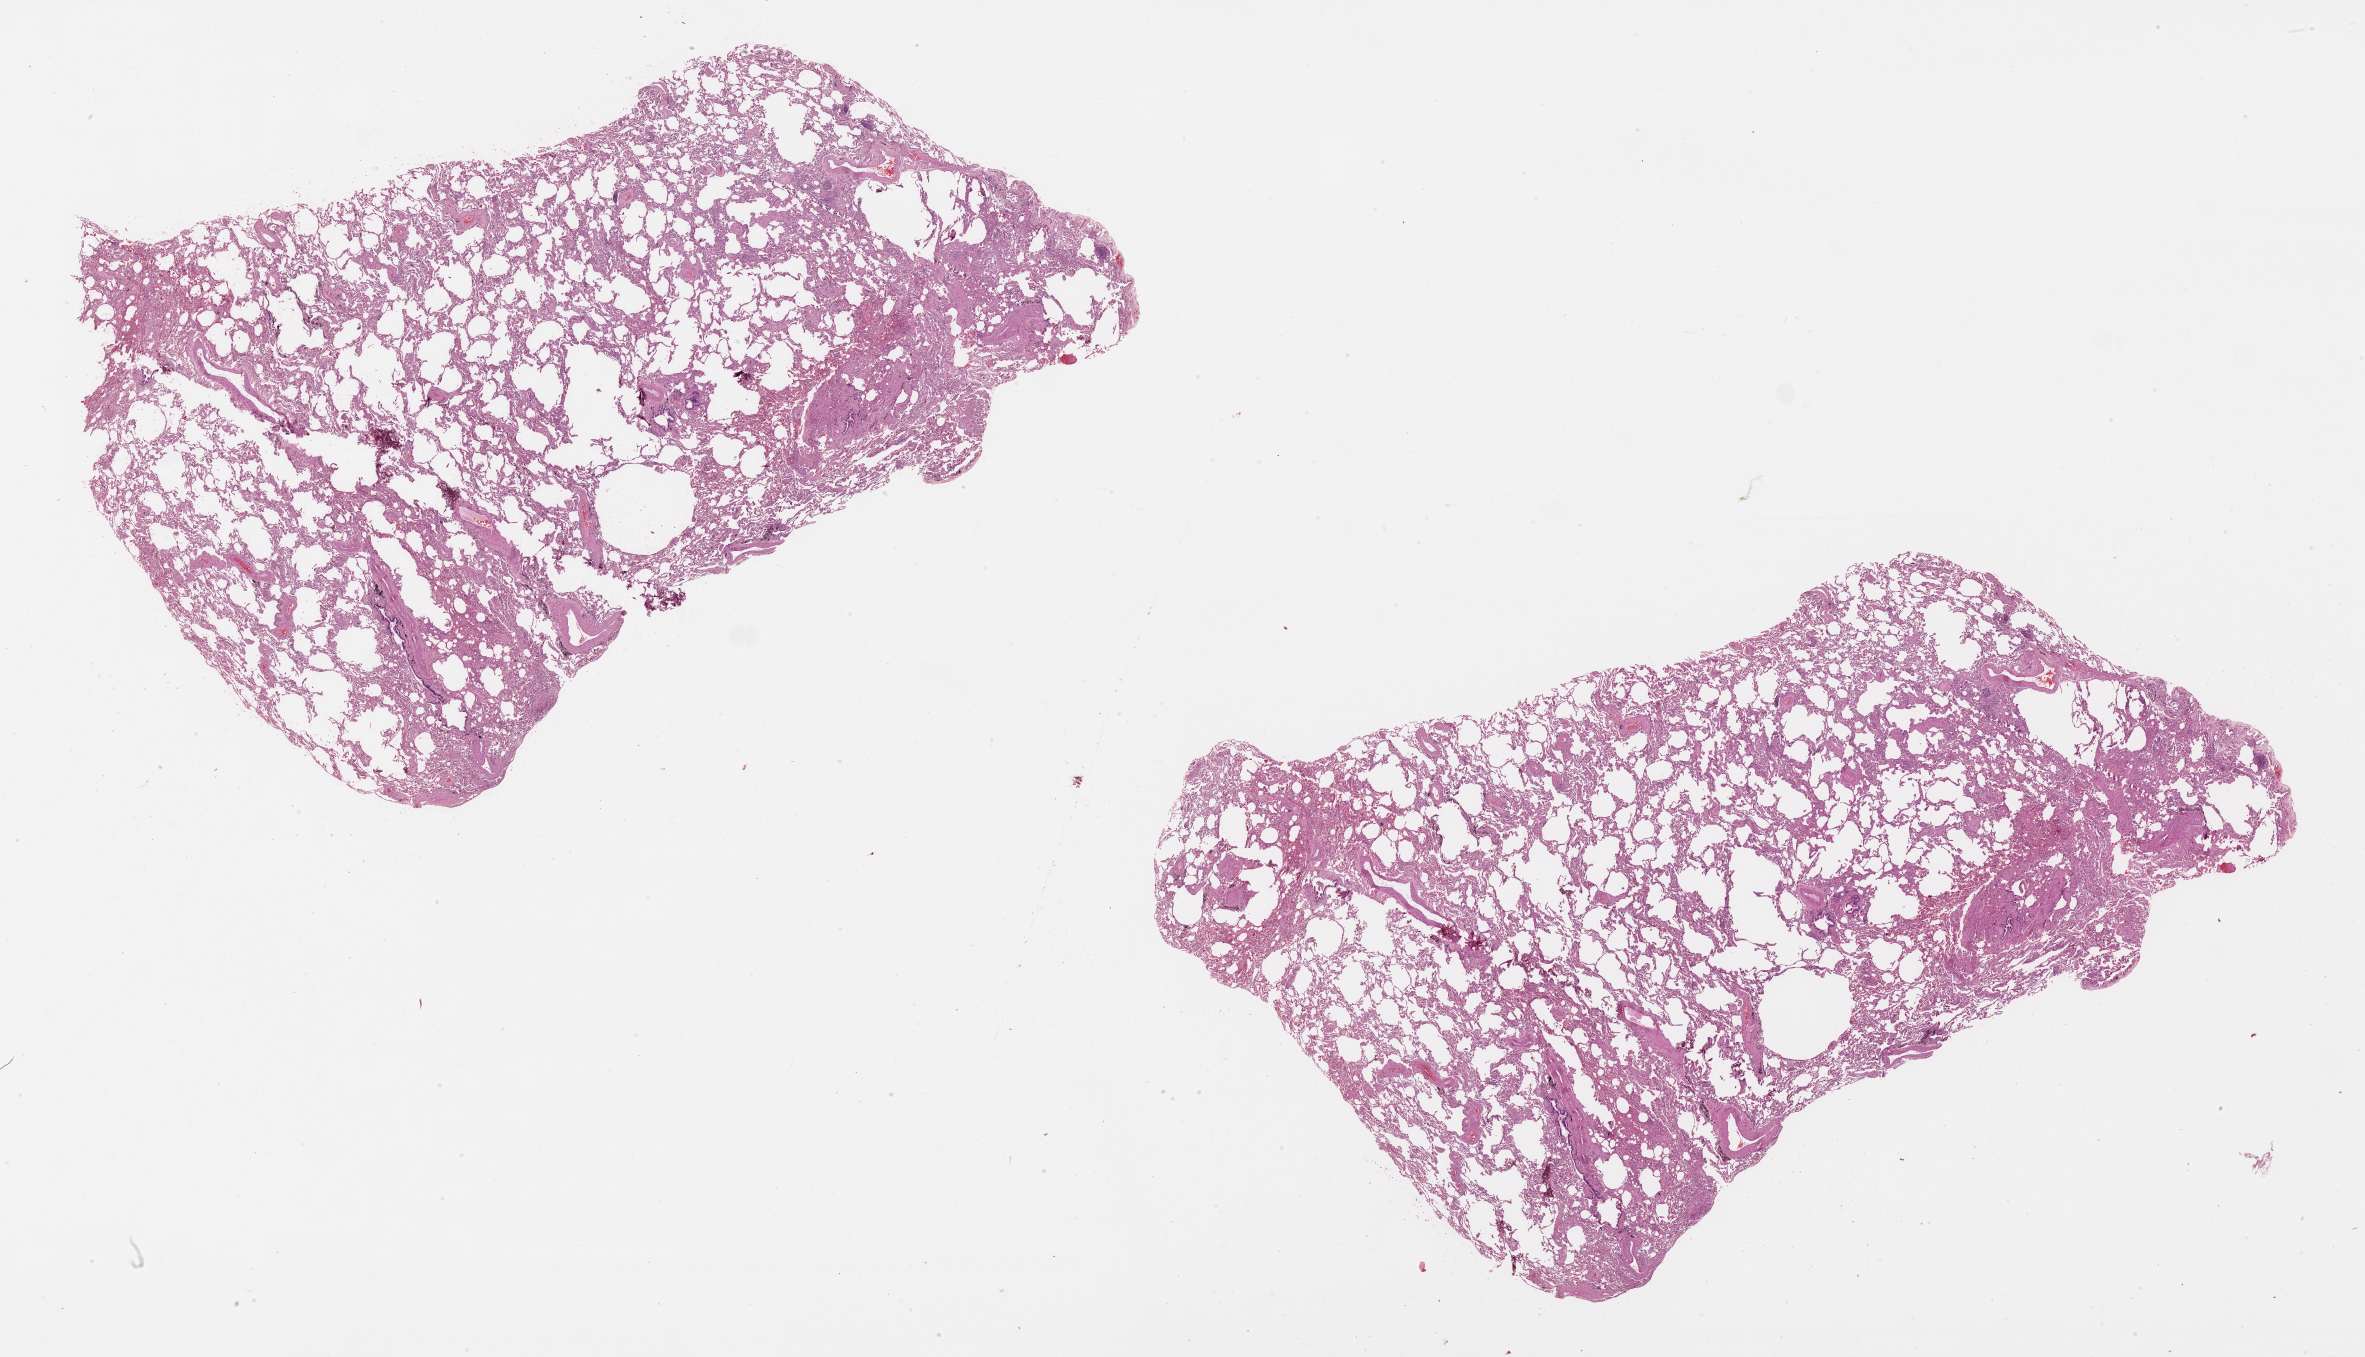
Whole-slide histology image, H&E-stained, low-resolution overview of the scanned area, about 38.1 x 21.9 mm (acquisition: 20x scan). Lung, normal (non-tumour) tissue. 77-year-old male patient.
This section: normal (non-tumour) tissue from the same patient. Patient diagnosis (cohort enrolment): squamous cell carcinoma (lung).